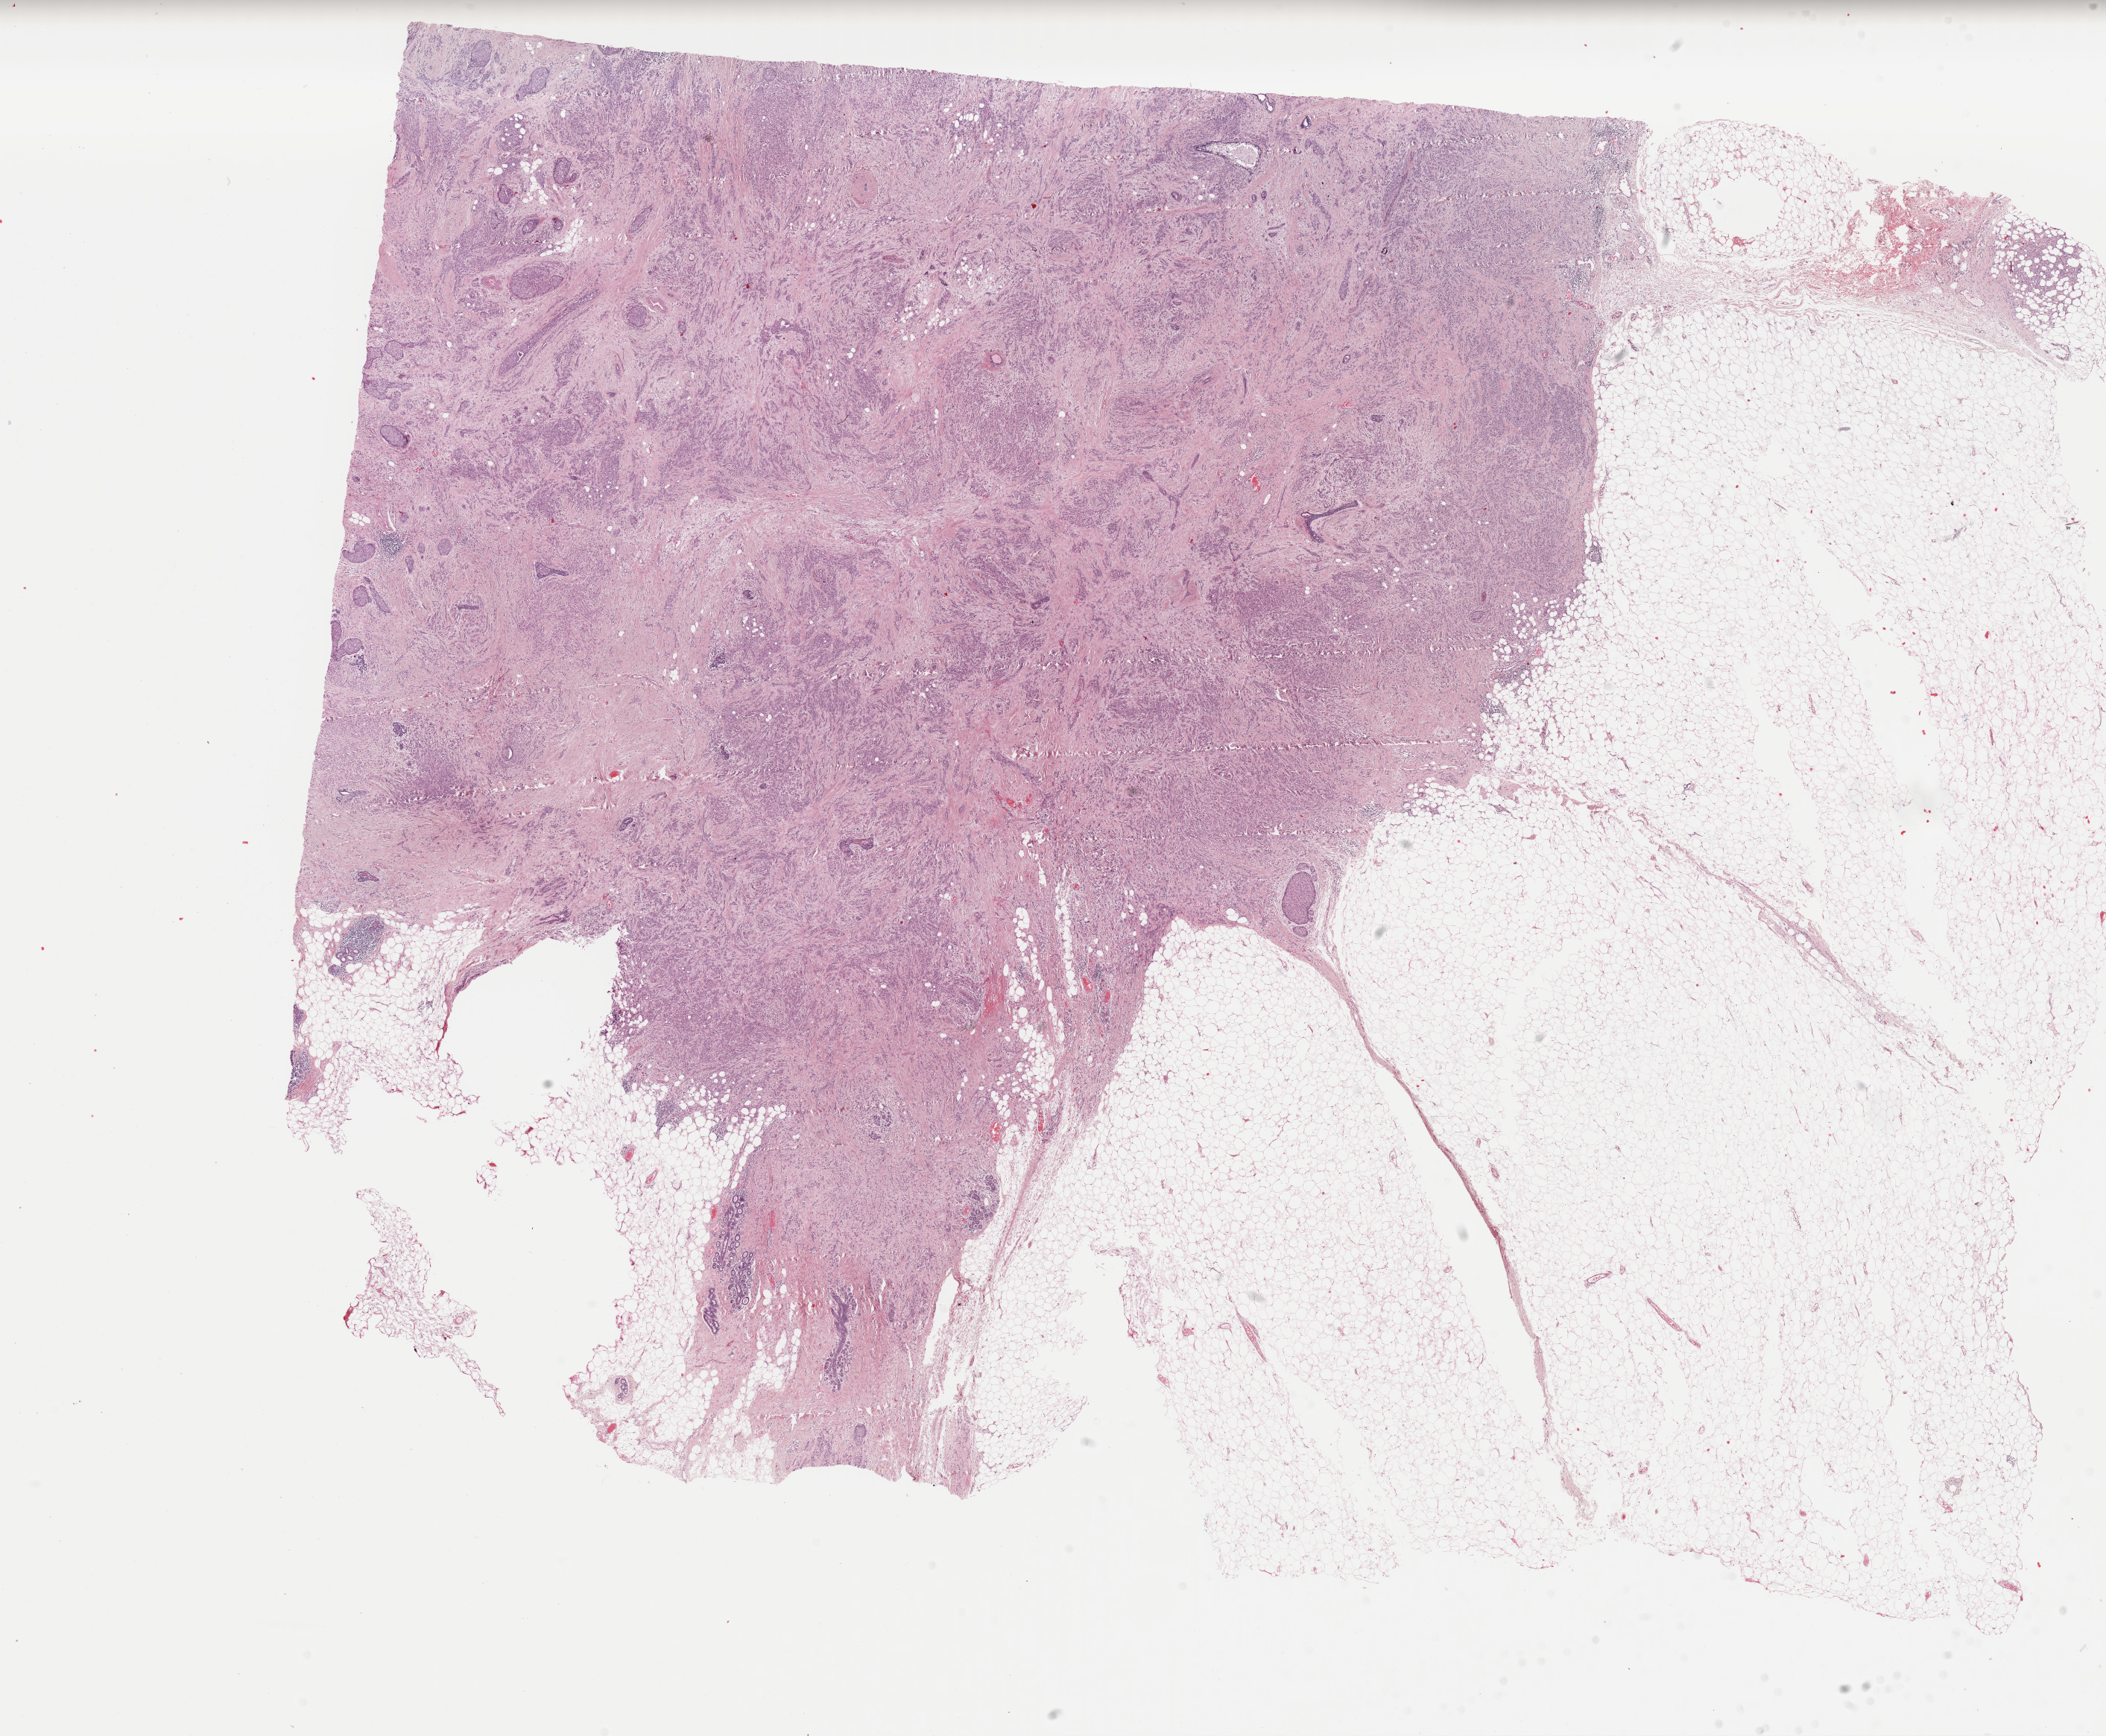
Digitized H&E tissue section (whole slide) — whole scanned area (about 22.3 x 18.4 mm, slide scanned at 40x) shown as a low-resolution overview; FFPE section; breast, primary tumour sample. Female, age 56 years at initial diagnosis.
- pathologic diagnosis: Lobular carcinoma, NOS
- laterality: left
- lymph nodes positive (case pathology): 19 of 22 examined
- TNM: T3 N3a M0
- AJCC pathologic stage: IIIC (7th edition)